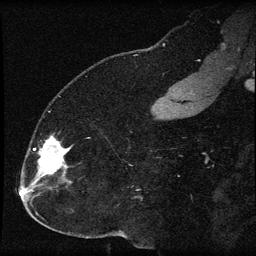
Breast MRI (dynamic contrast-enhanced), one sagittal slice. Position 25 of 60 along the scan axis. Dynamic contrast-enhanced series, image 2 of 3 at this slice position (ordered by acquisition). 1.5 T. TE 4.2 ms, TR 8.2 ms. 256 × 256 image matrix. Patient: female, 32 years.
Annotated regions visible in this slice (semi-automatic segmentation, software-assisted and operator-edited):
- analysis volume of interest (the breast-tissue region the enhancement analysis was run in; not a lesion): bounding box (x1, y1, x2, y2) in pixels: (31, 135, 72, 184)
- tumour enhancement mask (voxels above the 70 % enhancement threshold inside the analysis volume of interest): (33, 136, 71, 183)